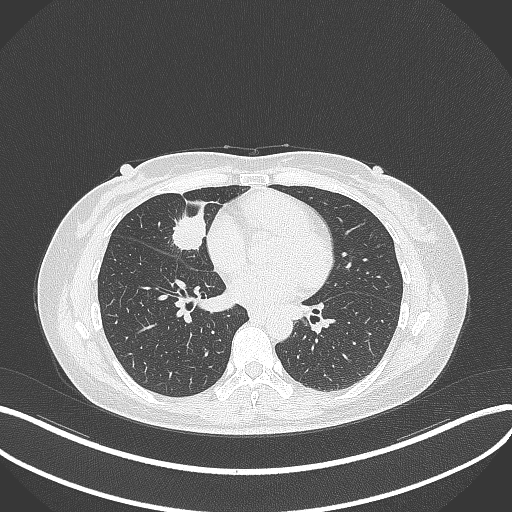
Chest CT, one axial slice. Slice 127 of 284 in the series (ordered by position). Reconstruction kernel B70f. Lung window (W 1500 / L -600 HU). 512 × 512 image matrix. Female patient, age 43 years. From the clinical record (not read from this slice): clinical TNM (as recorded): T1c N3 M1; histopathological grade: G1.
Outlined on this slice (bounding box drawn by a radiologist):
- lung tumour (recorded histology: adenocarcinoma): bounding box [x1, y1, x2, y2] px = [166, 200, 210, 253]